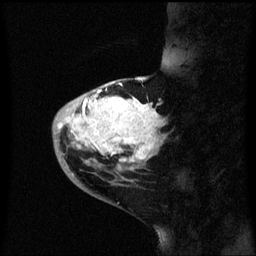
Breast MRI (dynamic contrast-enhanced), one sagittal slice. Position 19 of 60 along the scan axis. Dynamic contrast-enhanced series, image 2 of 3 at this slice position (ordered by acquisition). 1.5 T. TE 4.2 ms, TR 8.4 ms. 256 × 256 image matrix, field of view 200 × 200 mm. Patient: female, 46 years. Case-level facts recorded for this patient, not image findings: setting: breast cancer imaged before/during neoadjuvant chemotherapy; receptor status: HER2-positive.
Annotated regions visible in this slice (semi-automatically segmented with operator editing):
- analysis volume of interest (the breast-tissue region the enhancement analysis was run in; not a lesion): bounding box <52,86,167,171> (left, top, right, bottom; pixels)
- tumour enhancement mask (voxels above the 70 % enhancement threshold inside the analysis volume of interest): <58,90,163,163>